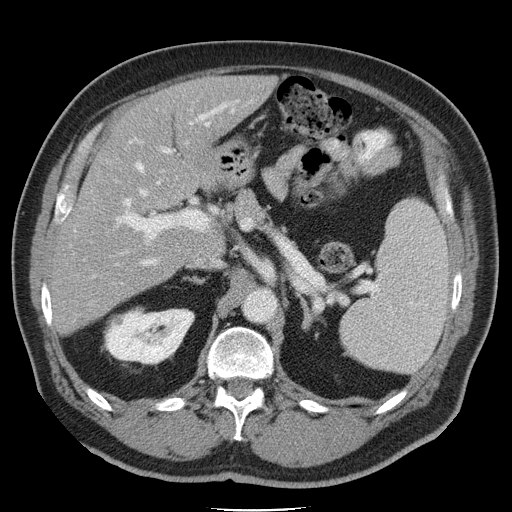
Contrast-enhanced abdominal CT, one axial slice. 120 kVp. Intravenous contrast given. Soft-tissue window (W 400 / L 40 HU). 5 mm slice thickness. 512 × 512 image matrix, field of view 386 × 386 mm. Male patient, age 65 years. From the clinical record (not read from this slice): diagnosis: colorectal cancer liver metastases, imaged before liver resection; multiple liver metastases: yes; largest metastasis: 4.9 cm; disease in both lobes: no.
Outlined on this slice (manually delineated by an expert):
- hepatic veins: box from (x=135, y=108) to (x=235, y=265) px
- liver: (x=51, y=76)–(x=272, y=329)
- planned liver remnant (the part of the liver to remain after resection): (x=104, y=77)–(x=272, y=243)
- portal vein (with intrahepatic branches): (x=114, y=103)–(x=229, y=249)